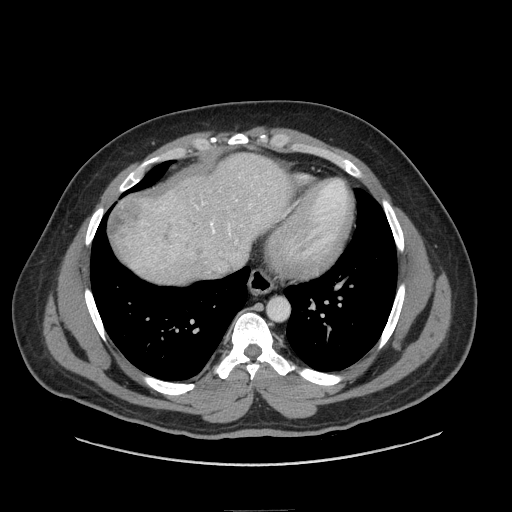
Contrast-enhanced abdominal CT (liver protocol), one axial slice. Slice 72 of 87 in the series (ordered by position). 140 kVp. Soft-tissue window (W 400 / L 40 HU). 2.5 mm slice thickness. 512 × 512 image matrix, field of view 440 × 440 mm. From the clinical record (not read from this slice): diagnosis: hepatocellular carcinoma (patient treated with transarterial chemoembolisation; whether this scan precedes or follows treatment is not stated here); TNM stage (as recorded): Stage-II.
Annotated regions visible in this slice (semi-automatic segmentation, software-assisted and operator-edited):
- abdominal aorta: bounding box (x1, y1, x2, y2) in pixels: (268, 298, 288, 320)
- liver parenchyma outside the tumour (the mass and vessels are separate outlines, so this box may not span the whole liver): (114, 154, 286, 284)
- mass: (108, 195, 183, 264)
- liver vessels: (210, 223, 230, 234)